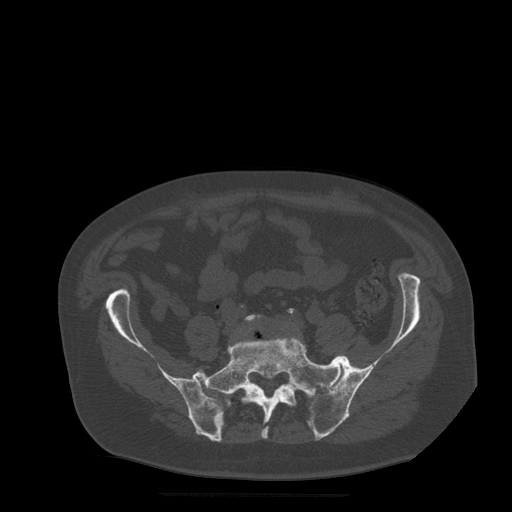
CT including the spine, one axial slice. Slice 68 of 522 in the series (ordered by position). Bone window (W 1800 / L 400 HU). 512 × 512 image matrix. Patient age 72 years. Case-level facts recorded for this patient, not image findings: primary cancer: prostate.
Outlined on this slice (semi-automatic segmentation, software-assisted and operator-edited):
- L5 vertebra: bounding box (x1, y1, x2, y2) in pixels: (245, 315, 263, 390)